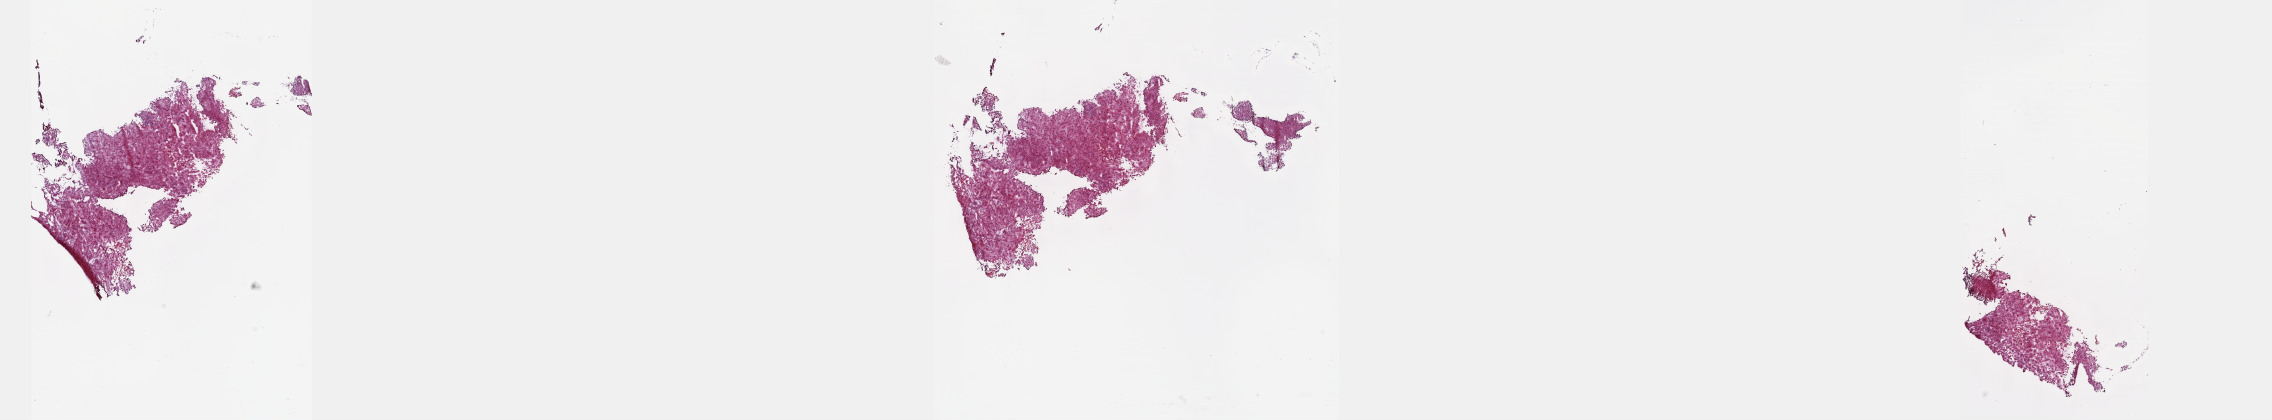
H&E whole-slide image, shown as a low-resolution overview of the whole scanned area (about 36.7 x 6.8 mm); frozen section from the top of the tissue portion; primary tumour sample from the cervix. Female patient; age at initial diagnosis 55 years. Histologic grade: G3 (poorly differentiated). Pathologist review of this section (percent, as recorded): tumour cells 80%, tumour nuclei 95%, normal cells 0%, stromal cells 20%, necrosis 0%. Inflammatory infiltration, as recorded: lymphocyte infiltration 0%, monocyte infiltration 0%, neutrophil infiltration 0%.
- diagnosis: Squamous cell carcinoma, NOS (cervix uteri)
- FIGO stage: IIIB